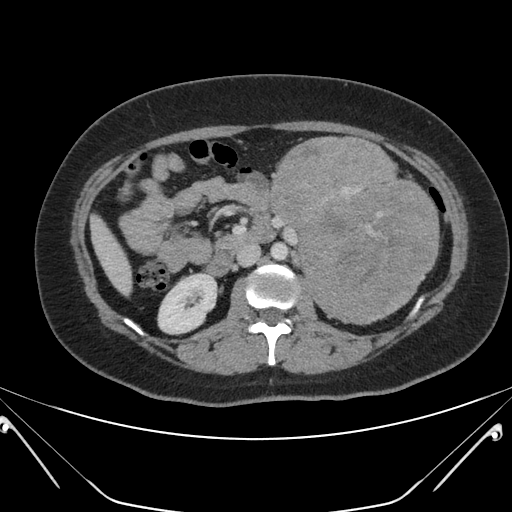
Contrast-enhanced abdominal CT, one axial slice. Slice 107 of 168 in the series (ordered by position). 120 kVp. Intravenous contrast given. Soft-tissue window (W 400 / L 40 HU). 3 mm slice thickness. 512 × 512 image matrix, field of view 394 × 394 mm. Female patient, age 26 years. From the clinical record (not read from this slice): diagnosis: adrenocortical carcinoma; tumour side: left adrenal; tumour size at pathology: 28 cm; Ki-67 index: 20 %; stage (as recorded): 2.
Annotated regions visible in this slice (semi-automatic segmentation, software-assisted and operator-edited):
- mass: bounding box <268,136,439,323> (left, top, right, bottom; pixels)